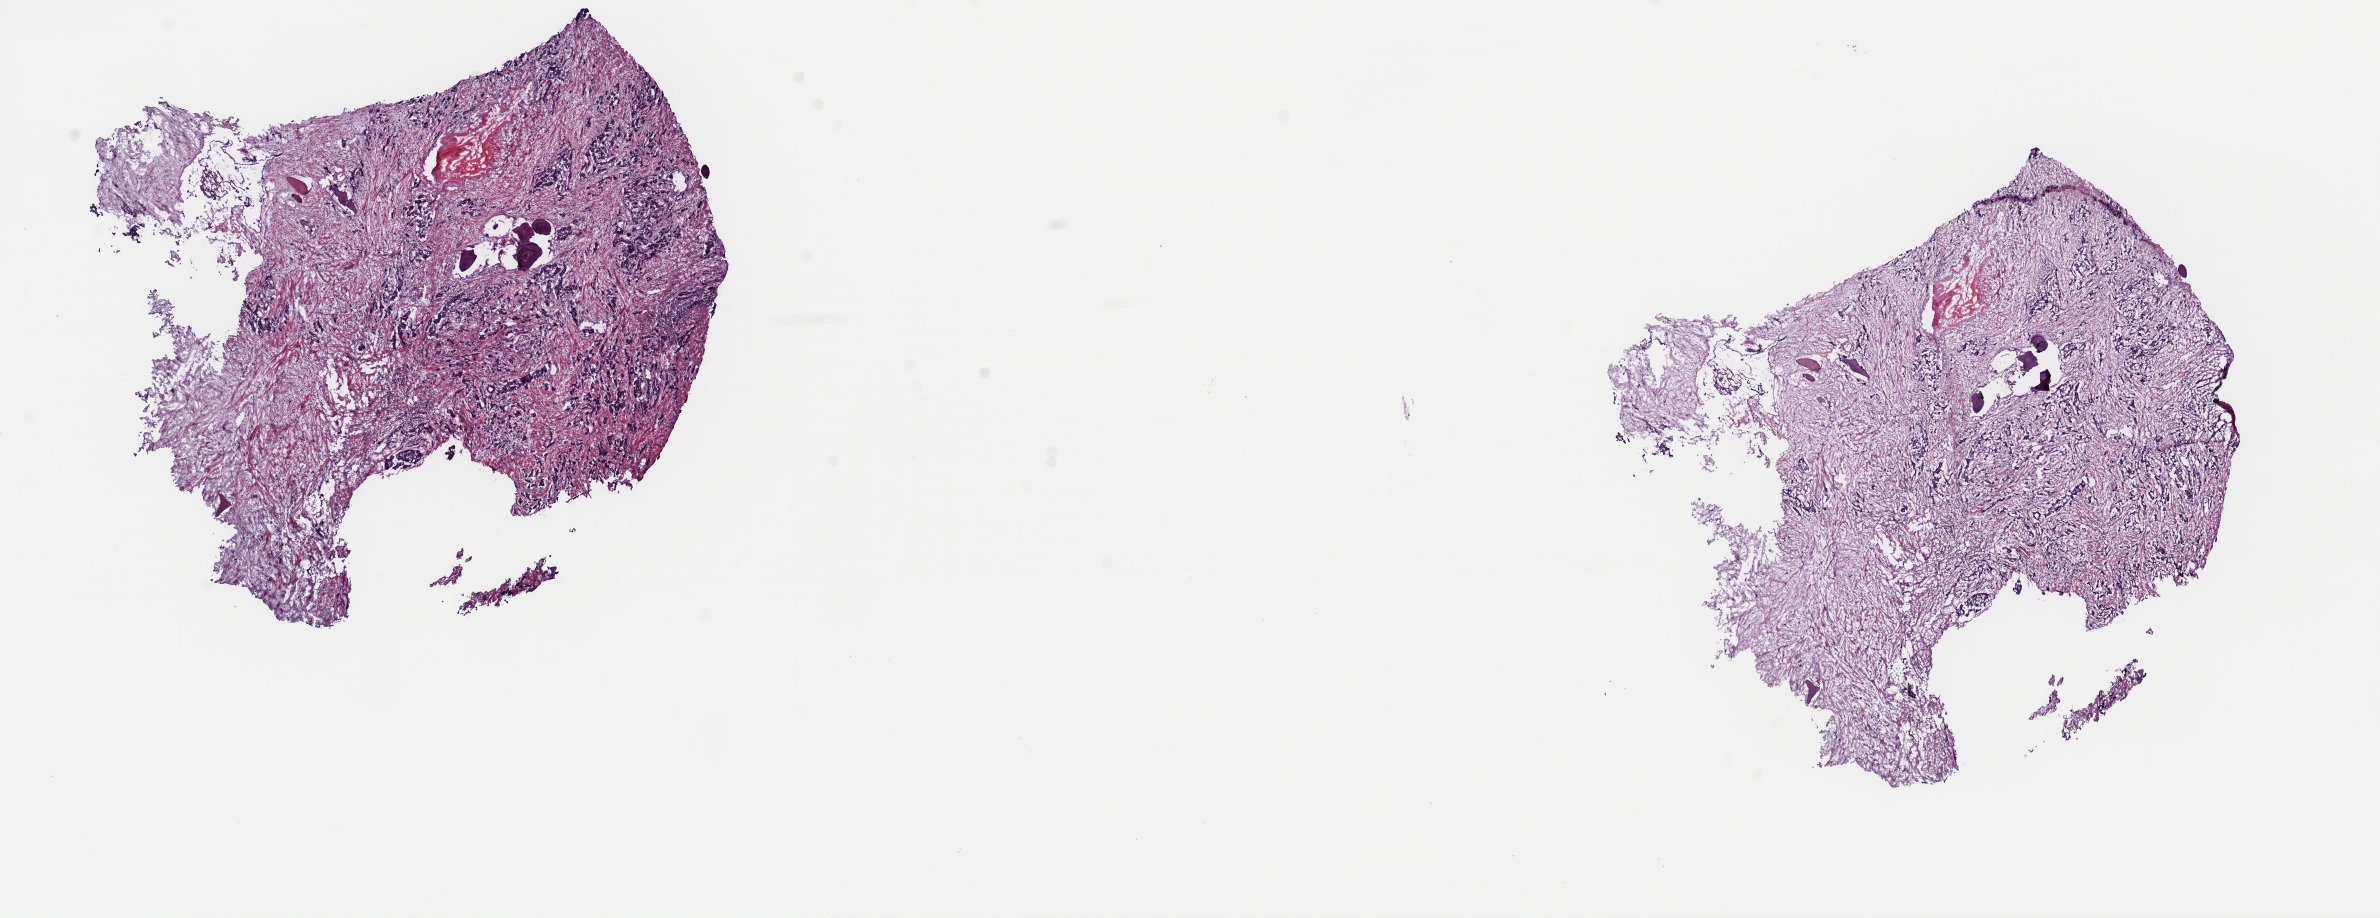
Digitized H&E-stained tissue section (whole slide), a low-resolution overview of the entire scanned area, about 18.8 x 7.2 mm (slide scanned at 40x), frozen section from the top of the tissue portion, primary tumour sample from the prostate. Male patient; age at initial diagnosis 64 years. Gleason score: 9 (4+5). Pathologist review of this section (percent, as recorded): tumour cells 70%, tumour nuclei 70%, normal cells 30%, stromal cells 0%, necrosis 0%. Inflammatory infiltration, as recorded: lymphocyte infiltration 0%, monocyte infiltration 0%, neutrophil infiltration 0%.
Histologic diagnosis: Acinar cell carcinoma (prostate gland).